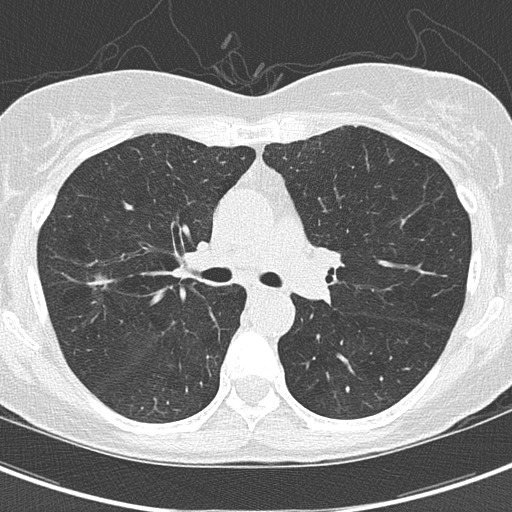
Axial slice from a low-dose chest CT screening exam. Third screening round (two years after baseline). Lung window (W 1500 / L -600 HU). 2 mm slice thickness. Lung (sharp) reconstruction kernel (B50f). 120 kVp. Slice 58 of 154 in the series. Female, age 59 years at enrolment.
Expert reader's lesion annotation, bounding box <71,261,131,316> (left, top, right, bottom; pixels). Reader record for this screening exam (exam-level; its link to the box is not recorded): non-calcified nodule or mass ≥4 mm, right upper lobe, 10 × 8 mm, poorly defined margins, ground glass attenuation, pre-existing on the prior screen: yes; interval growth: yes. Official screen result: positive, other. Later outcome: lung cancer diagnosed 63 days after this screen — bronchiolo-alveolar adenocarcinoma, NOS, right upper lobe, well differentiated (G1), stage IA (AJCC 6th edition), 4 mm at pathology.